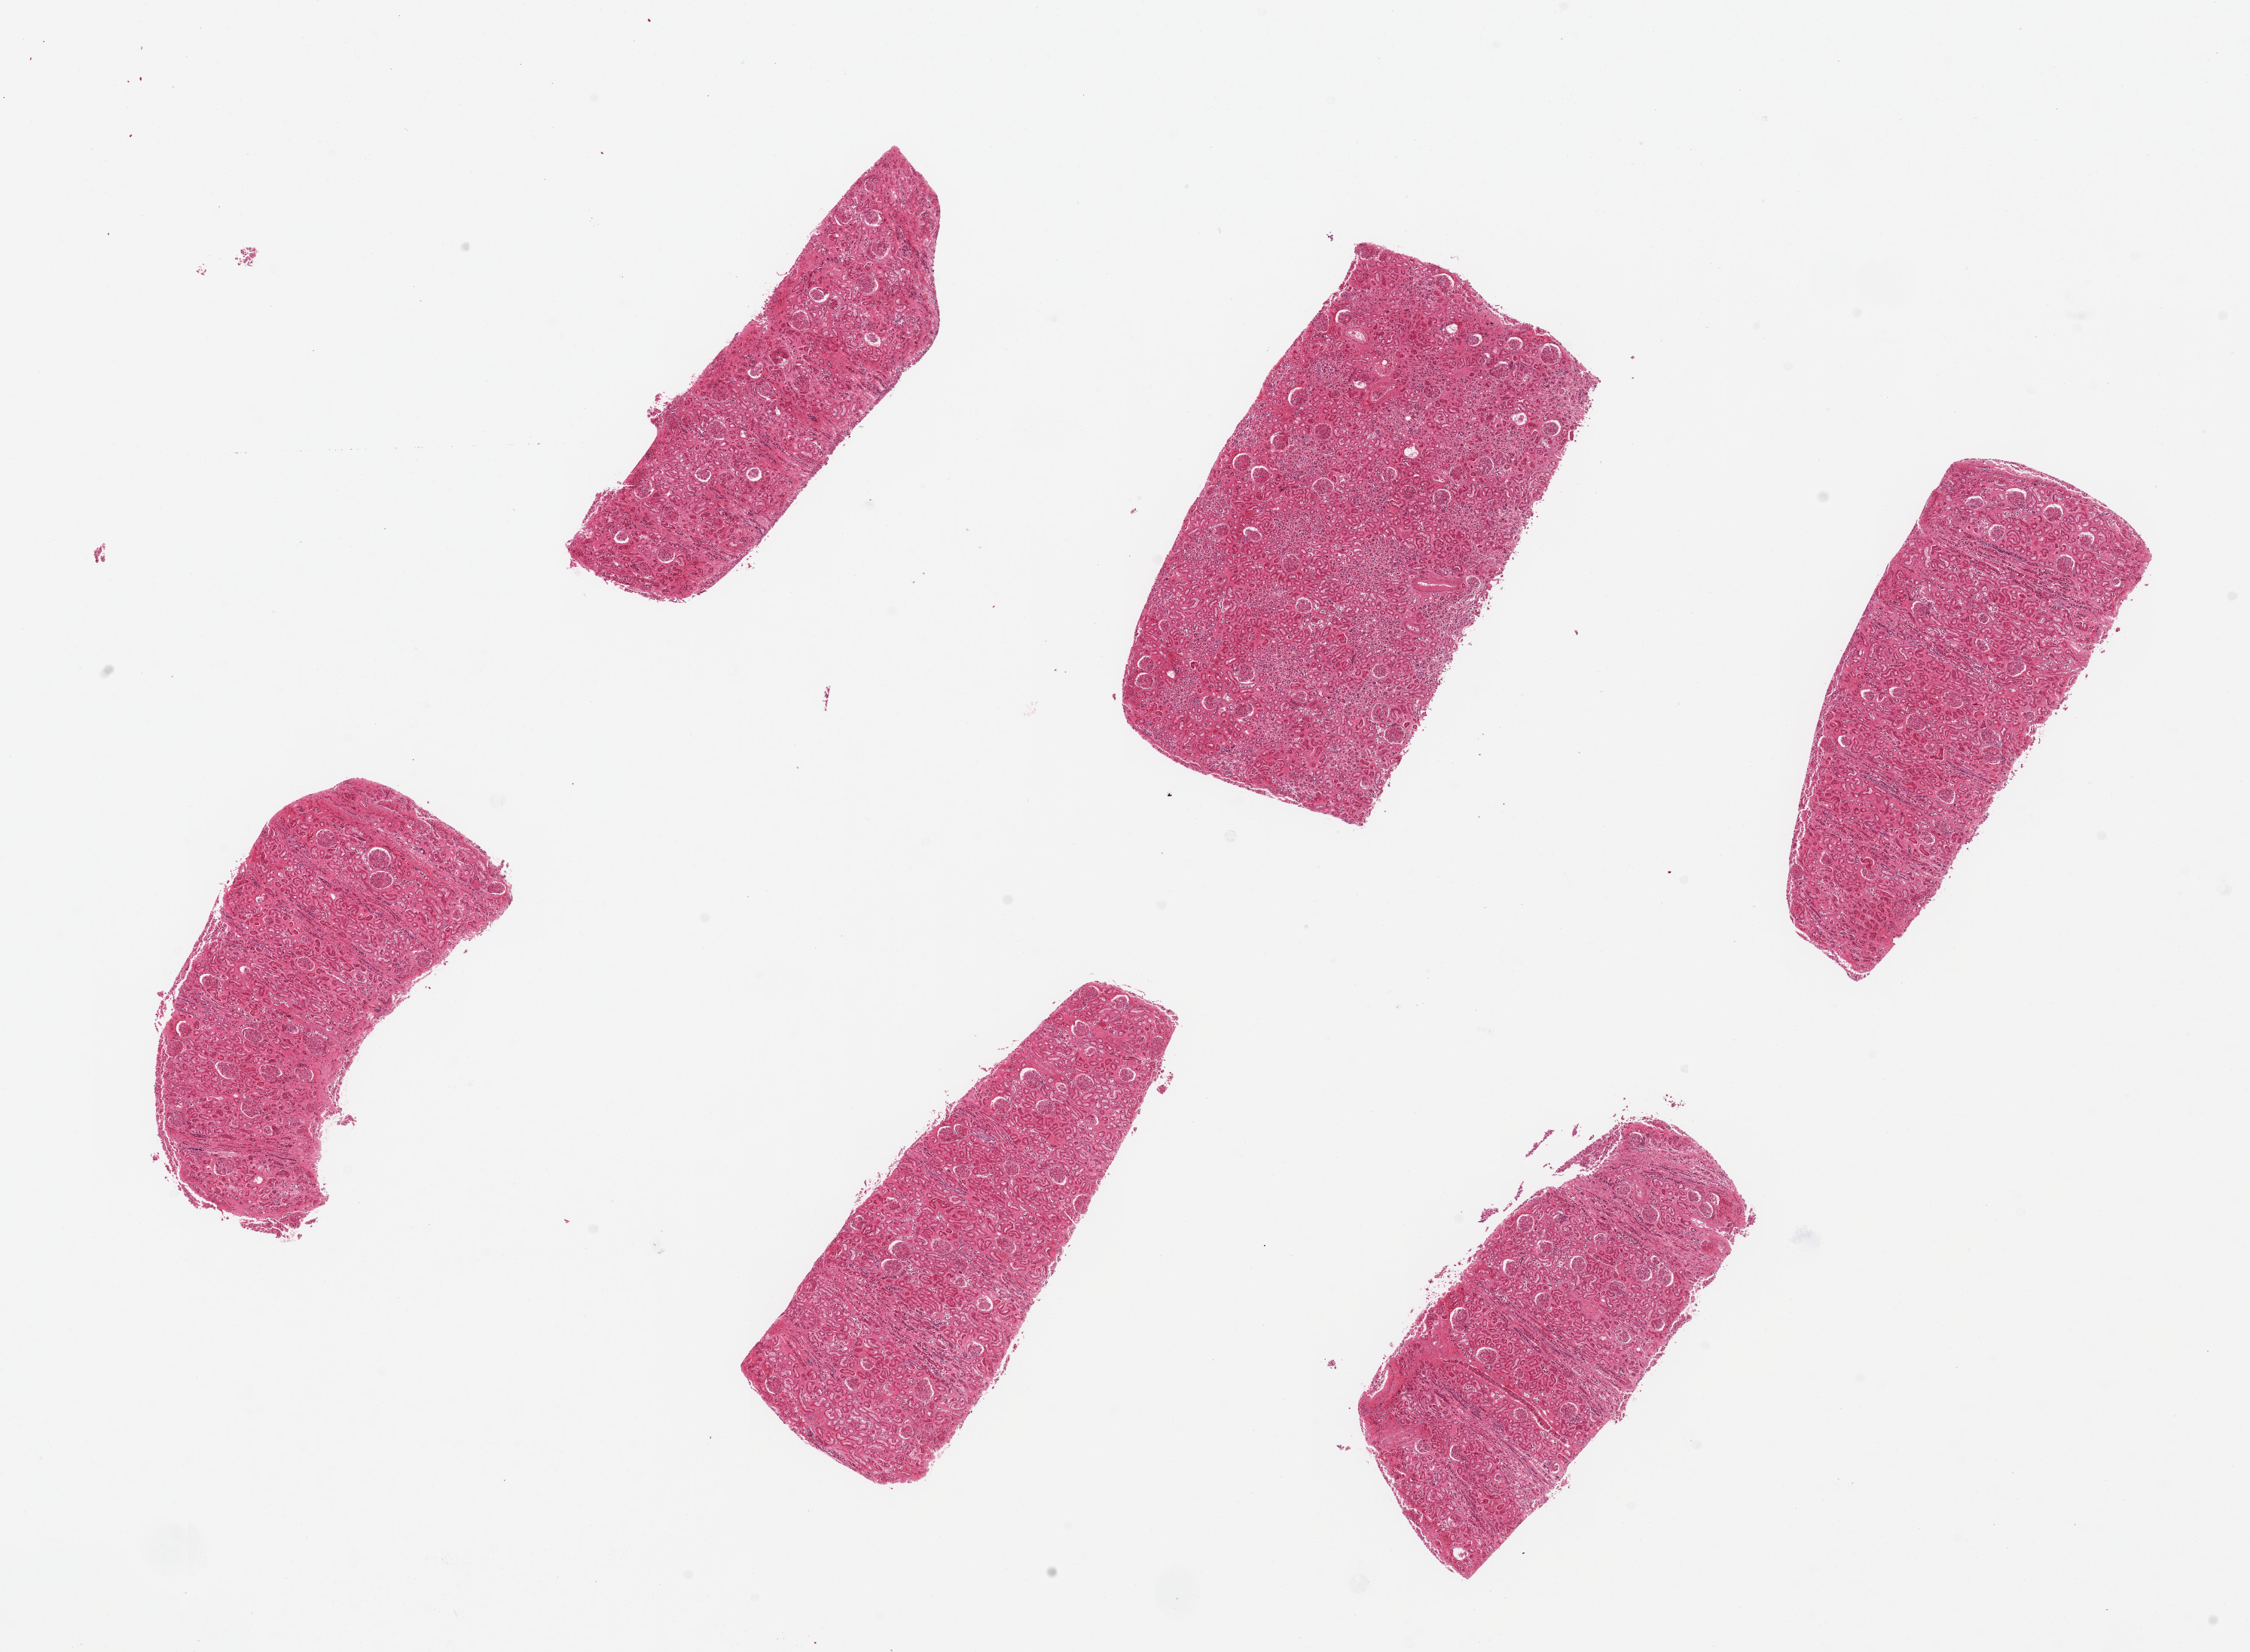
H&E whole-slide image, low-resolution overview of the scanned area, about 23.6 x 17.3 mm (slide scanned at 20x); PAXgene-fixed paraffin-embedded (PFPE) section; target tissue: renal cortex; tissue donor sample.
Reviewer comment on this tissue sample: 6 pieces ~6x2mm. Badly autolyzed.